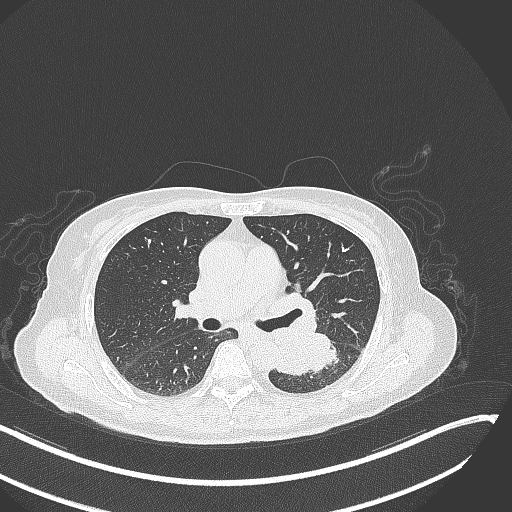
Chest CT, one axial slice; slice 163 of 342 in the series (ordered by position); 120 kVp; lung window (W 1500 / L -600 HU); 1 mm slice thickness; 512 × 512 image matrix. Patient: female, 64 years. Case-level facts recorded for this patient, not image findings: clinical TNM (as recorded): T3 N1 M1.
Structures marked on this image (bounding box drawn by a radiologist):
- lung tumour (recorded histology: small cell carcinoma): box from (x=271, y=335) to (x=349, y=375) px